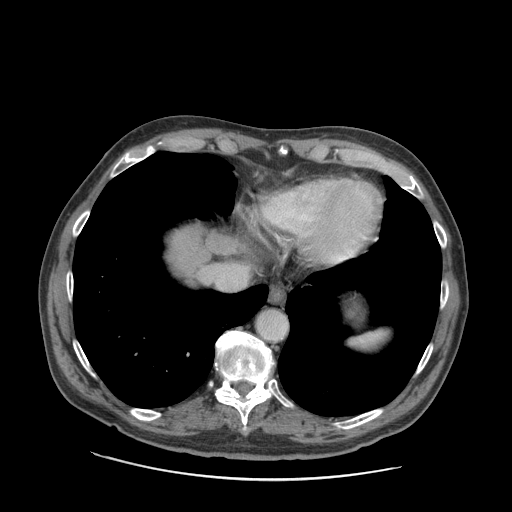
Contrast-enhanced abdominal CT (liver protocol), one axial slice; slice 80 of 89 in the series (ordered by position); reconstruction kernel STANDARD; 140 kVp; soft-tissue window (W 400 / L 40 HU); 2.5 mm slice thickness; 512 × 512 image matrix, field of view 420 × 420 mm. Case-level facts recorded for this patient, not image findings: diagnosis: hepatocellular carcinoma (patient treated with transarterial chemoembolisation; whether this scan precedes or follows treatment is not stated here); TNM stage (as recorded): Stage-I; Child-Pugh class: A.
Structures marked on this image (semi-automatic segmentation, software-assisted and operator-edited):
- liver parenchyma outside the tumour (the mass and vessels are separate outlines, so this box may not span the whole liver): box from (x=167, y=228) to (x=238, y=276) px